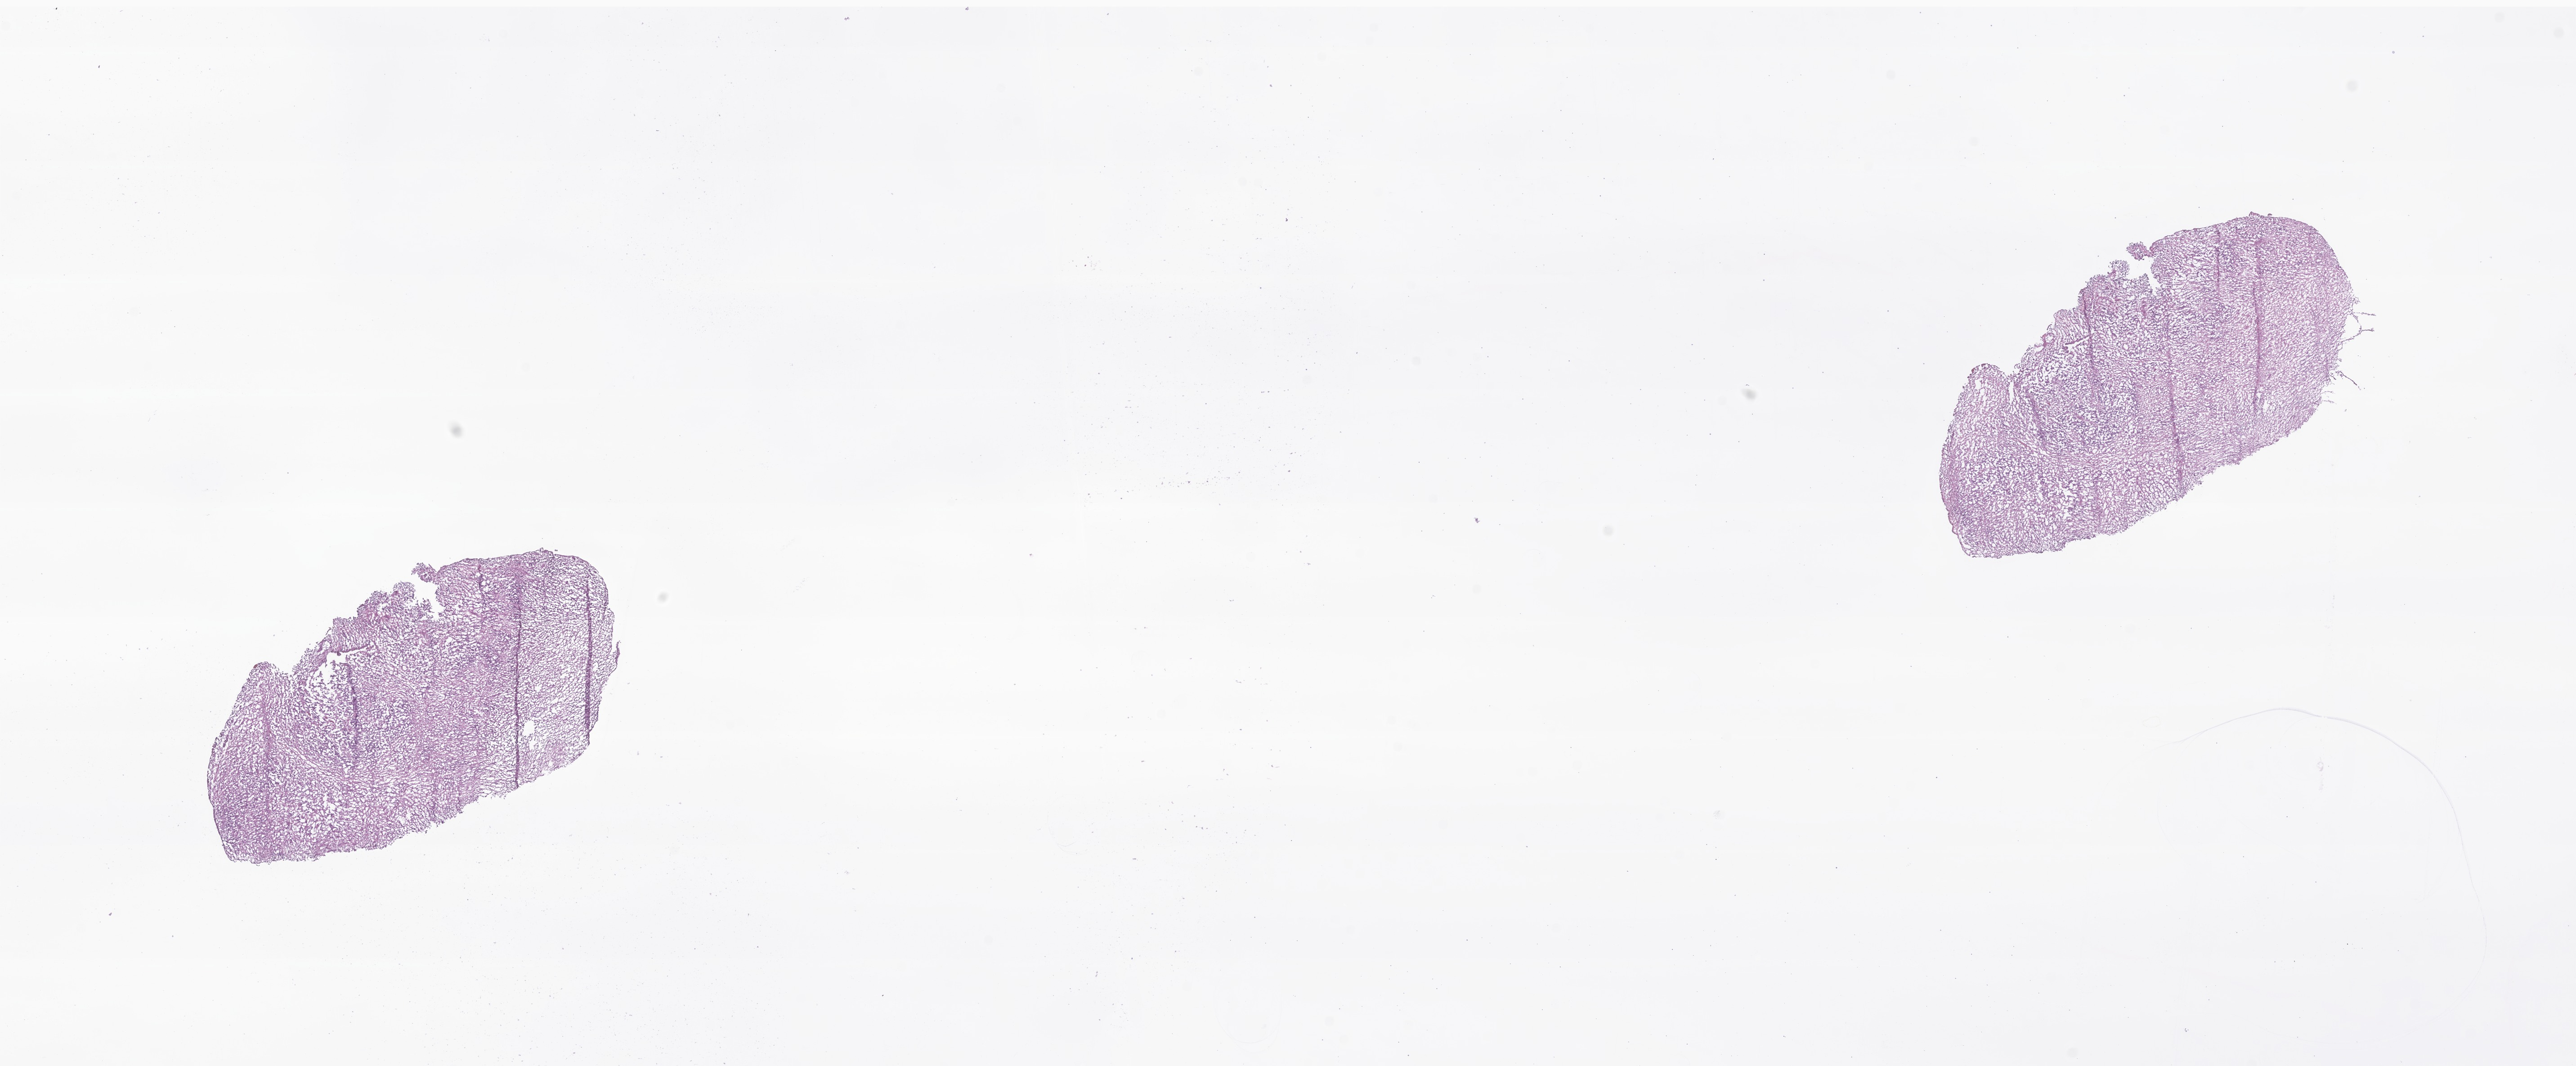
Haematoxylin and eosin whole-slide image of tumor tissue from the brain — low-resolution overview of the scanned area, about 24.1 x 10.0 mm; cryosection (OCT / tissue freezing medium). Patient: male, age 359 days.
Diagnosis (ICD-O-3 morphology term): Ependymoma, NOS.